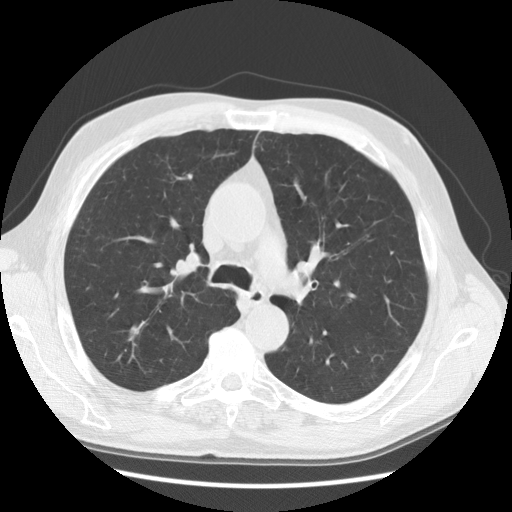
Chest CT (low-dose screening protocol), one axial image. Baseline annual screen. Lung window (W 1500 / L -600 HU). 2.5 mm slice thickness. Standard (soft-tissue) reconstruction kernel (STANDARD). 140 kVp. Male, age 60 years at enrolment. Current smoker at enrolment.
Expert reader's lesion annotation, bounding box [x1, y1, x2, y2] px = [162, 234, 218, 285]. No non-calcified nodule or mass ≥4 mm was recorded by the screening reader at this exam. Official screen result: negative screen, minor abnormalities not suspicious for lung cancer. Participant outcome: lung cancer diagnosed 193 days after this screen — squamous cell carcinoma, NOS, right upper lobe, moderately differentiated (G2), stage IIIB (AJCC 6th edition), 52 mm at pathology.